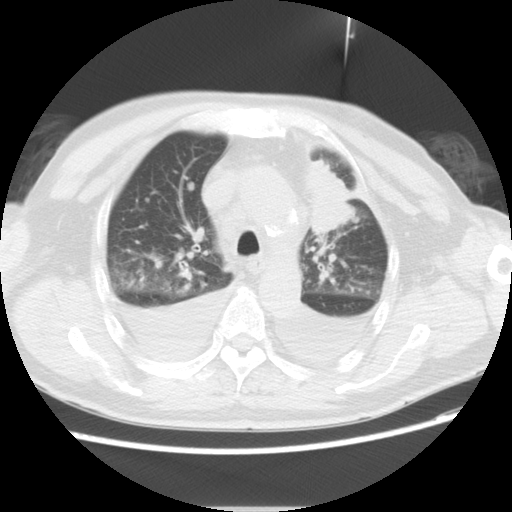
Chest CT, one axial slice; position 16 of 19 along the scan axis; 120 kVp; lung window (W 1500 / L -600 HU); 5 mm slice thickness; 512 × 512 image matrix, field of view 350 × 350 mm. Patient: male, 66 years. From the clinical record (not read from this slice): clinical TNM (as recorded): T1c N0 M0.
Structures marked on this image (rectangle marked by the reading radiologist):
- lung tumour (recorded histology: adenocarcinoma): bounding box (x1, y1, x2, y2) in pixels: (304, 155, 357, 235)